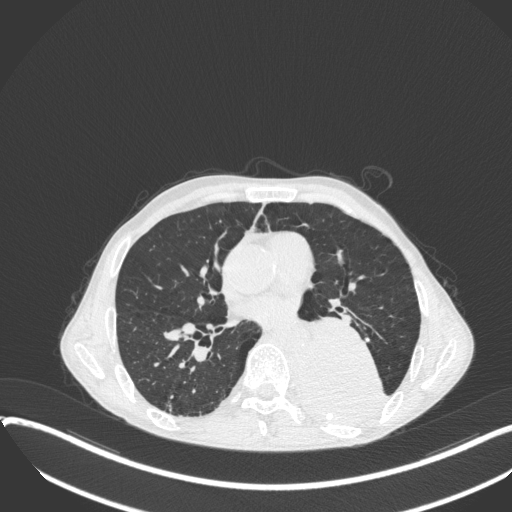
Chest CT, one axial slice. Position 186 of 400 along the scan axis. Reconstruction kernel B31f. 120 kVp. Lung window (W 1500 / L -600 HU). 1 mm slice thickness. 512 × 512 image matrix, field of view 400 × 400 mm. Male patient, age 57 years. Case-level facts recorded for this patient, not image findings: clinical TNM (as recorded): T4 N0 M0.
Outlined on this slice (bounding box drawn by a radiologist):
- lung tumour (recorded histology: squamous cell carcinoma): bounding box (x1, y1, x2, y2) in pixels: (295, 312, 392, 430)